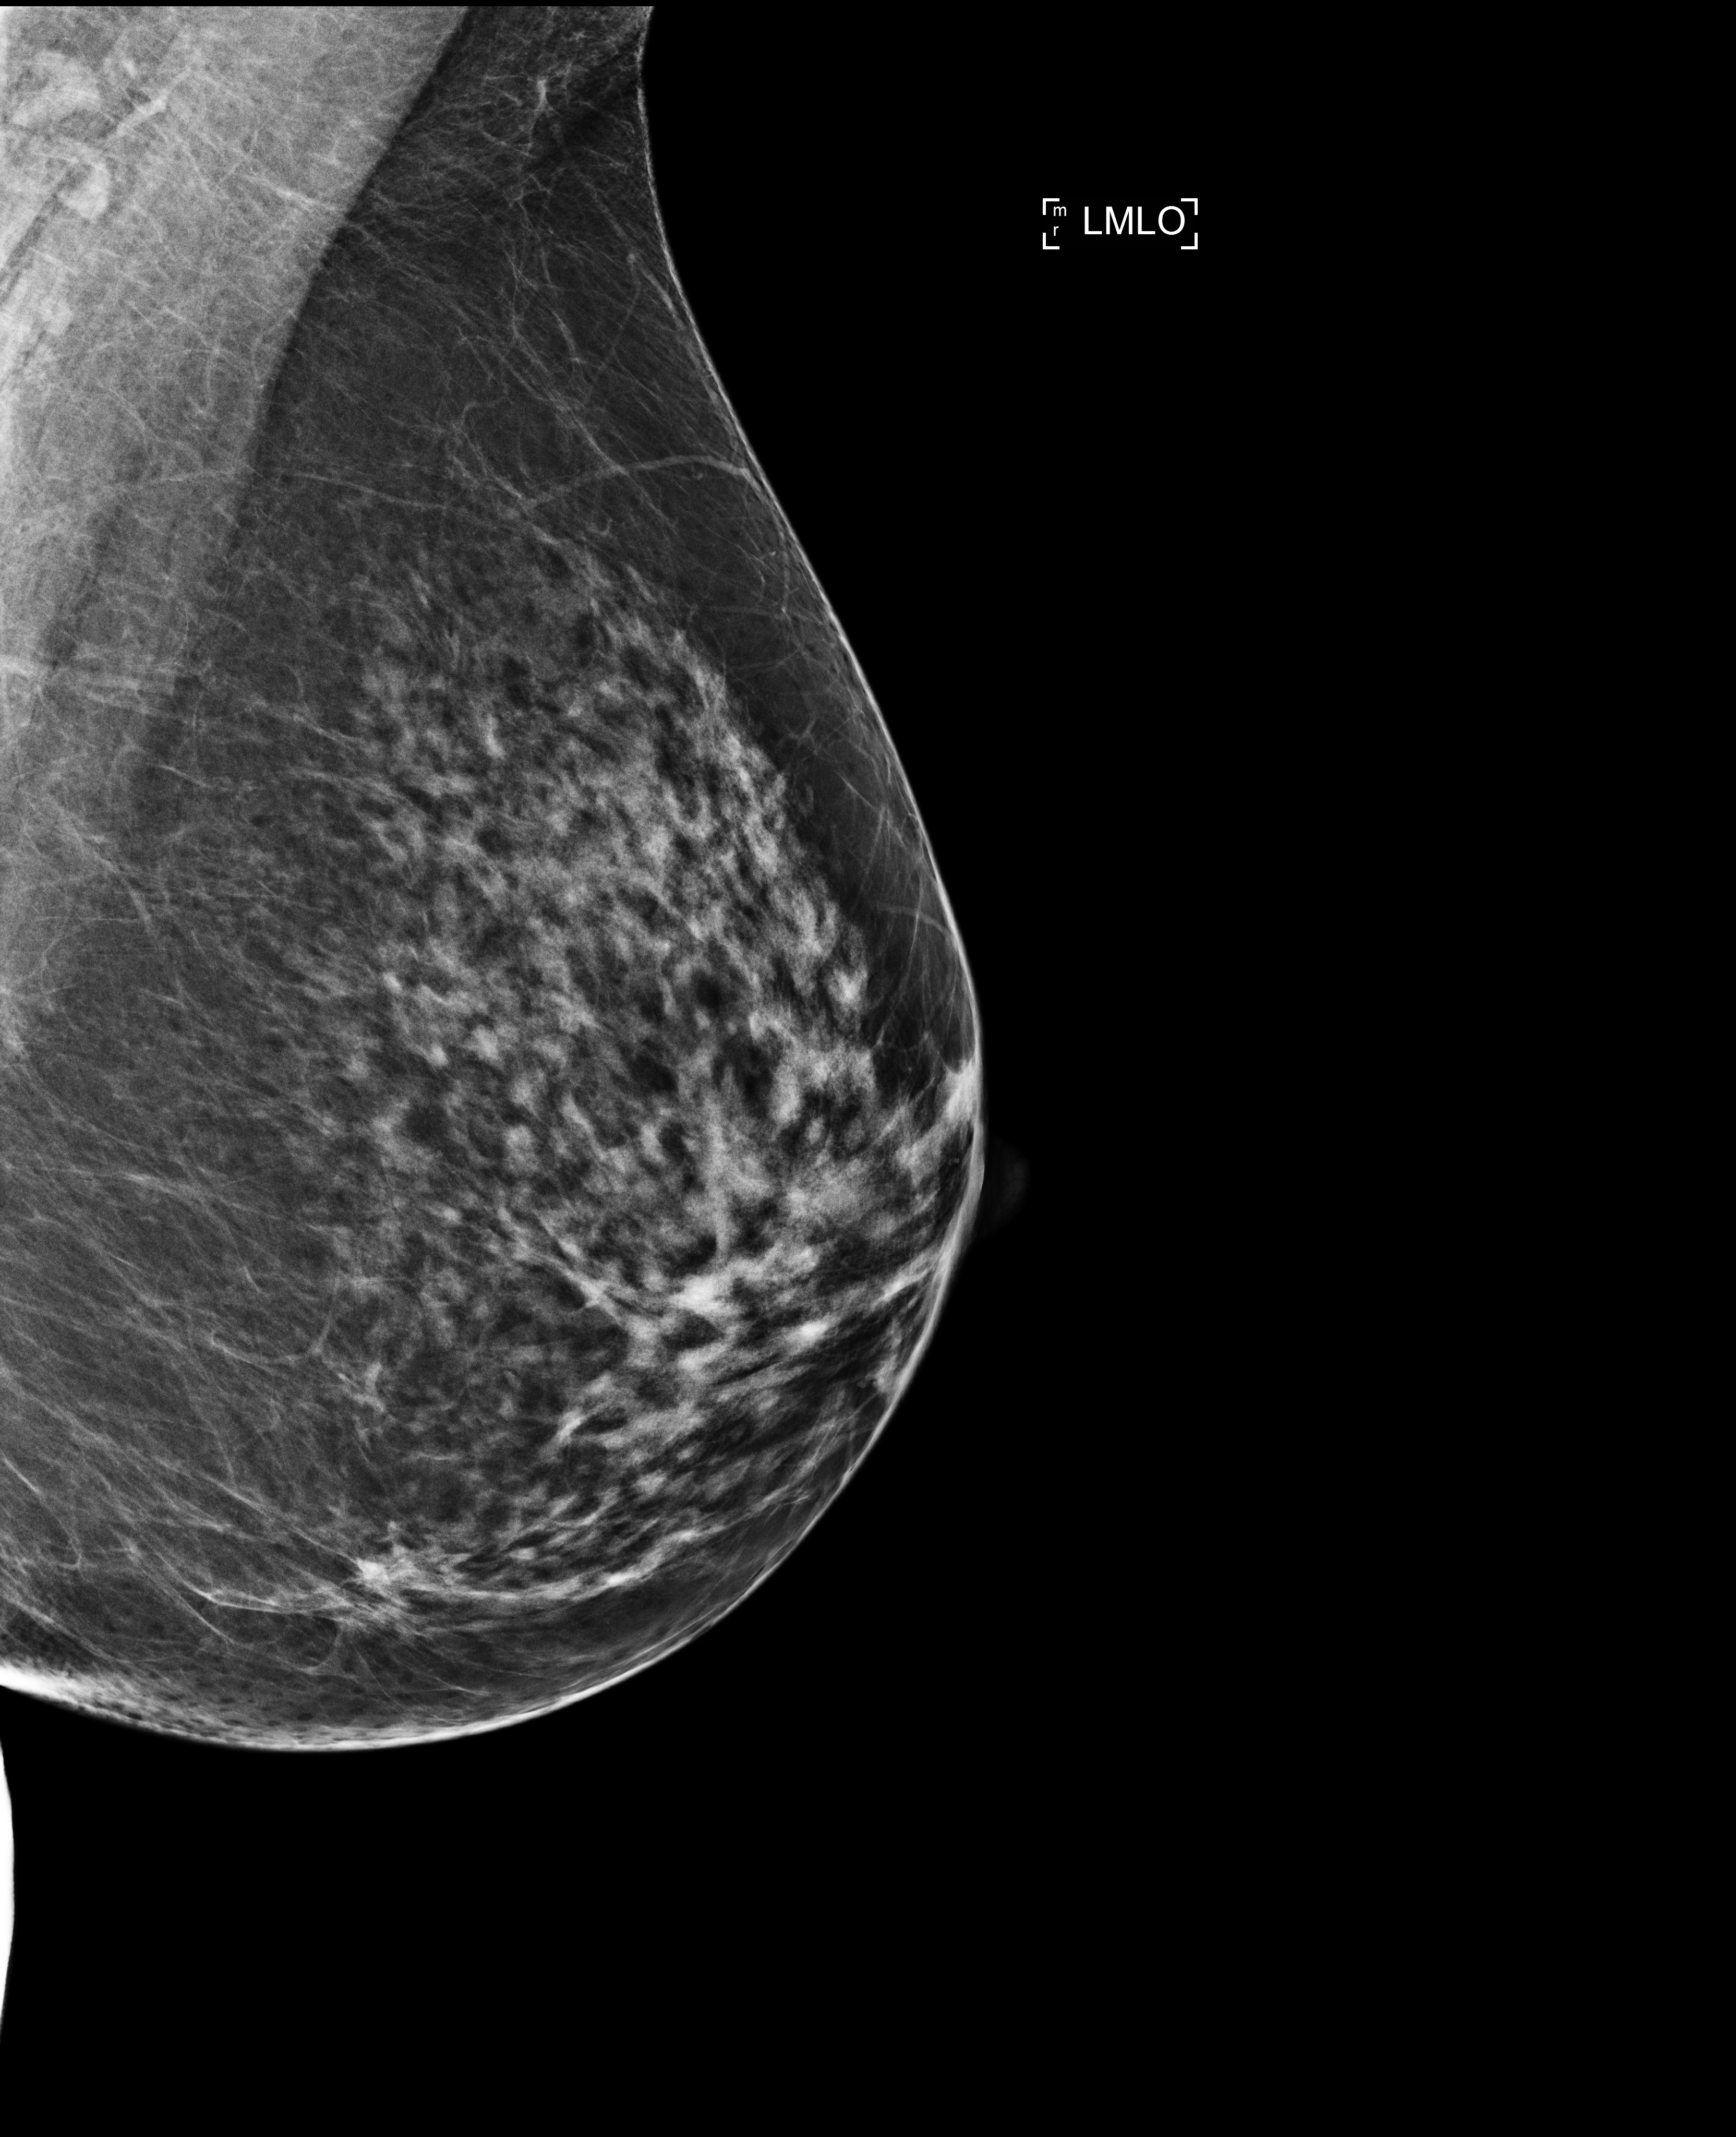
Annual screening mammography examination. Patient aged 53 years (female).
Image type: full-field digital mammogram. Breast: left. Projection: MLO view.